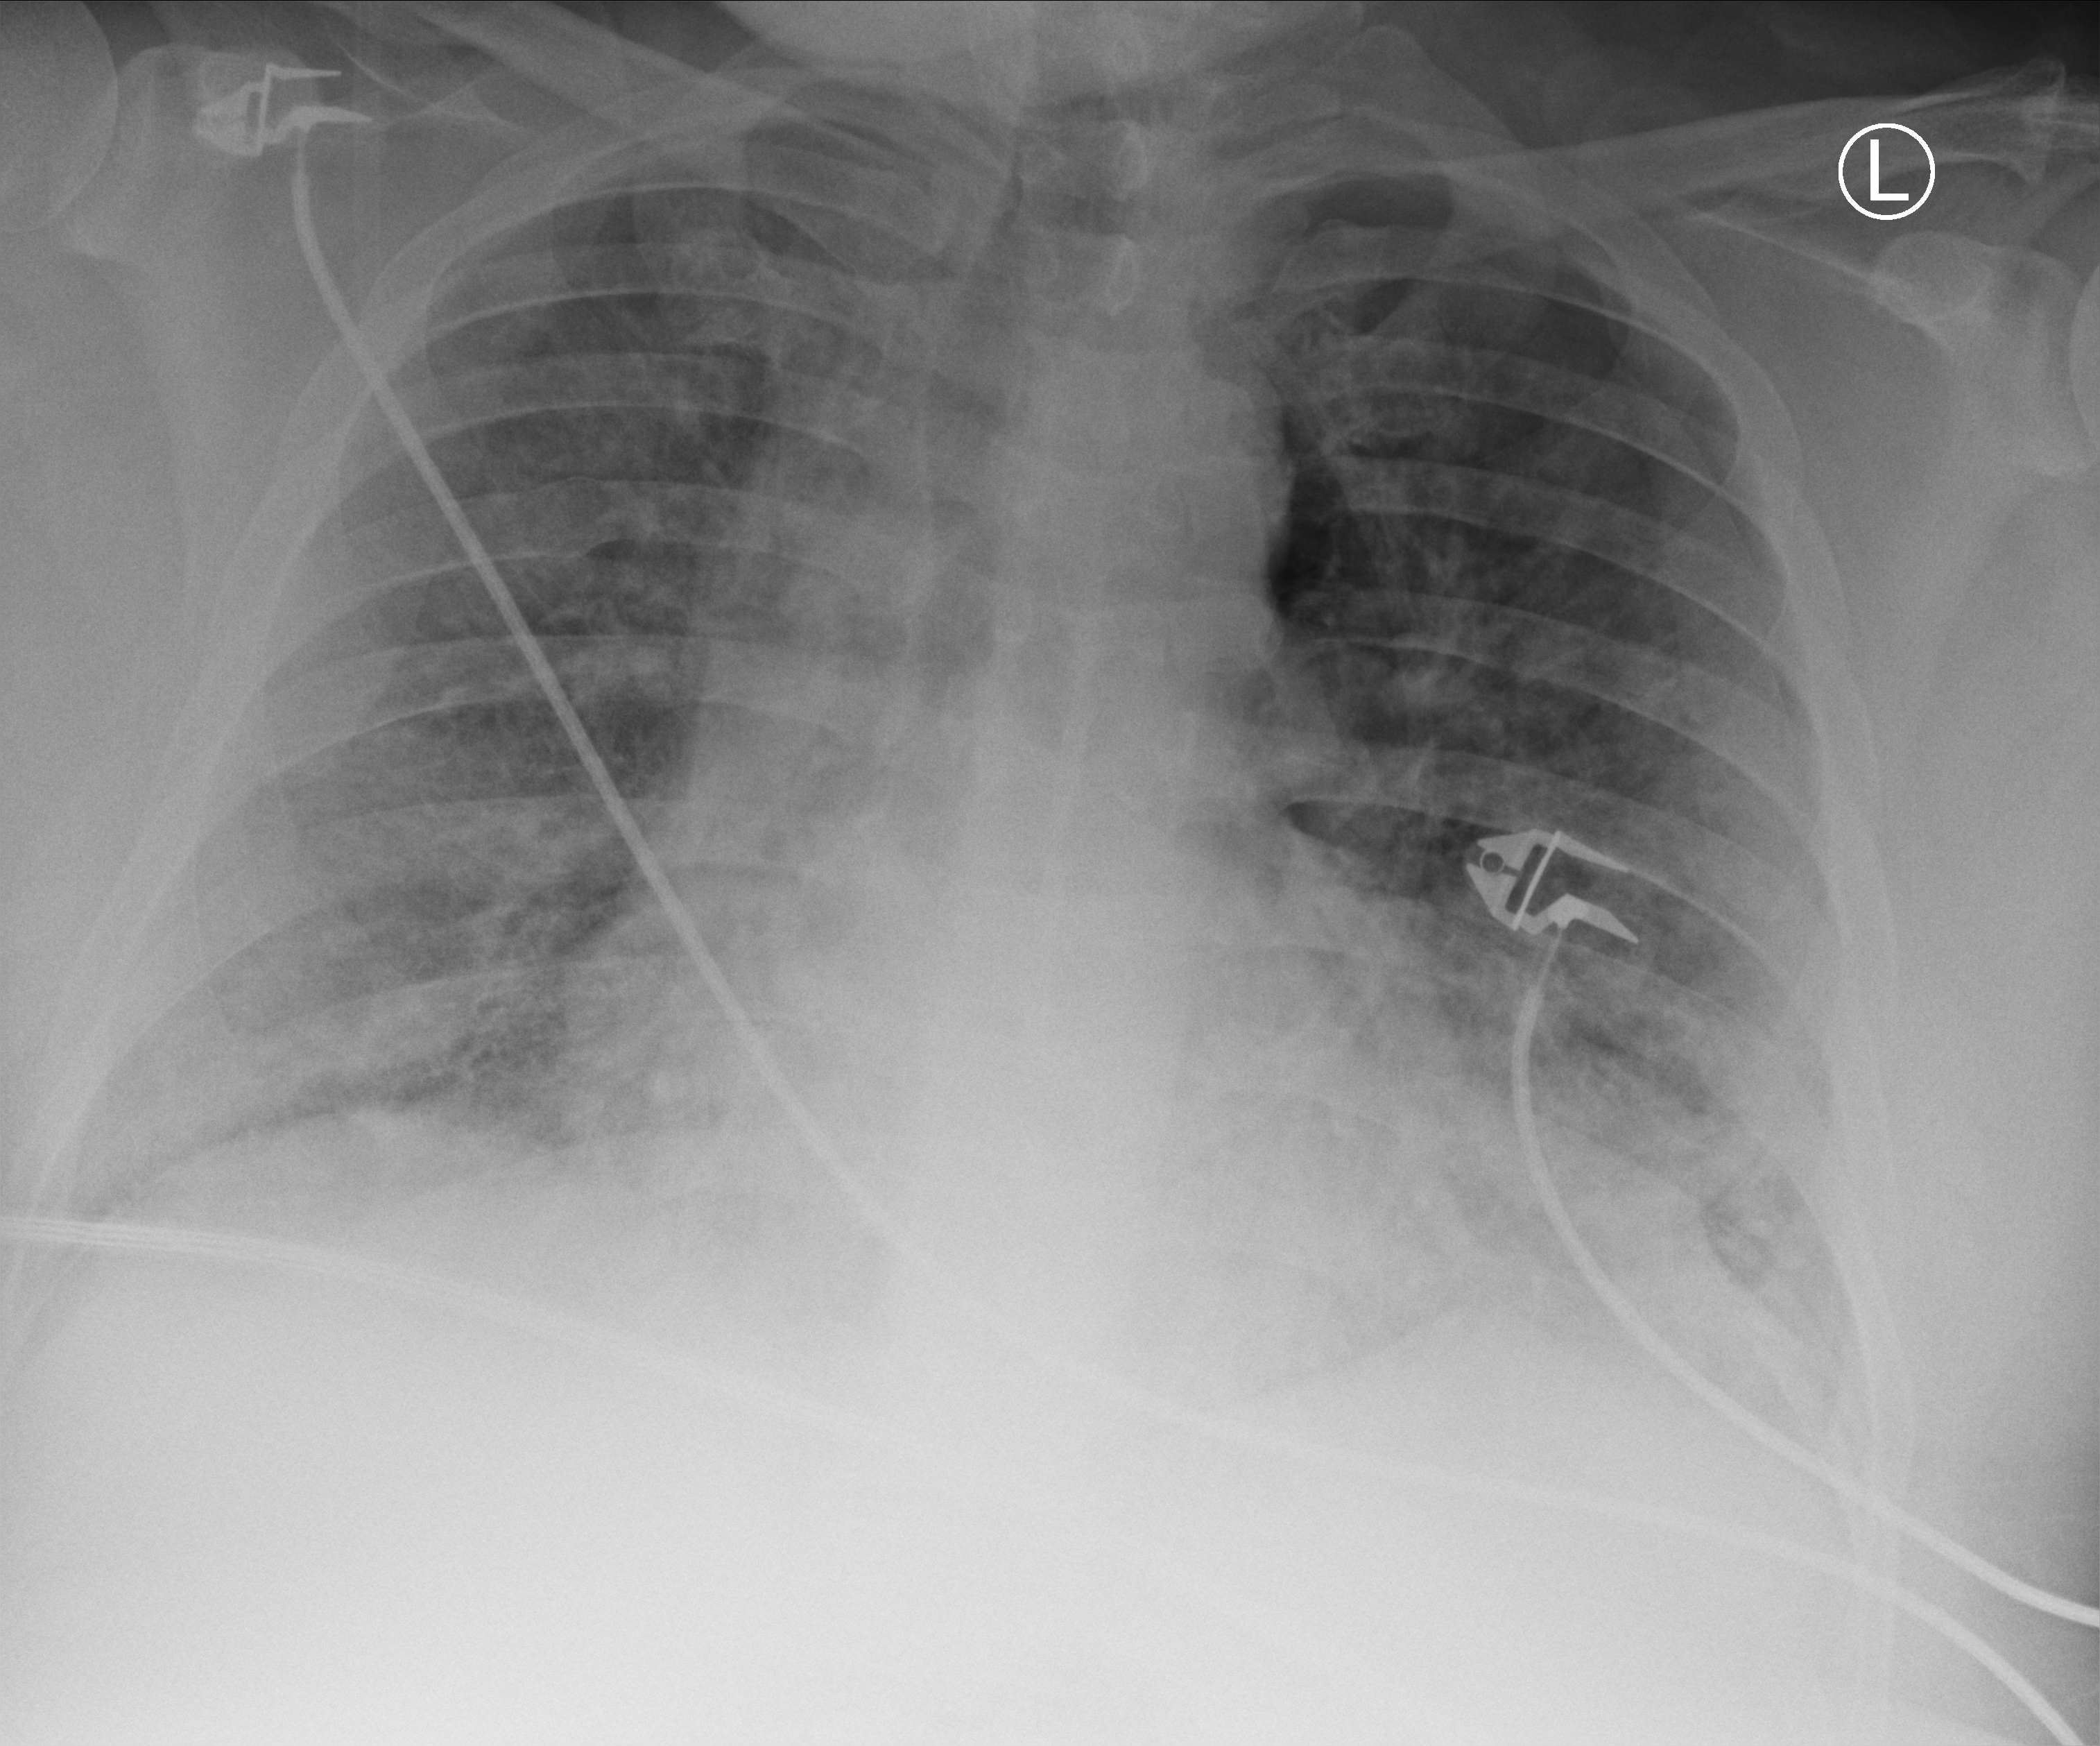
Portable chest radiograph; anteroposterior (AP) projection. Patient hospitalised with COVID-19; male, aged 18–59 years.
From the hospital-stay record, not from the radiograph (when in the stay this image was taken is not recorded): mechanically ventilated during this hospital stay: no; hypertension (admission record): yes; admitted to intensive care during this hospital stay: yes.